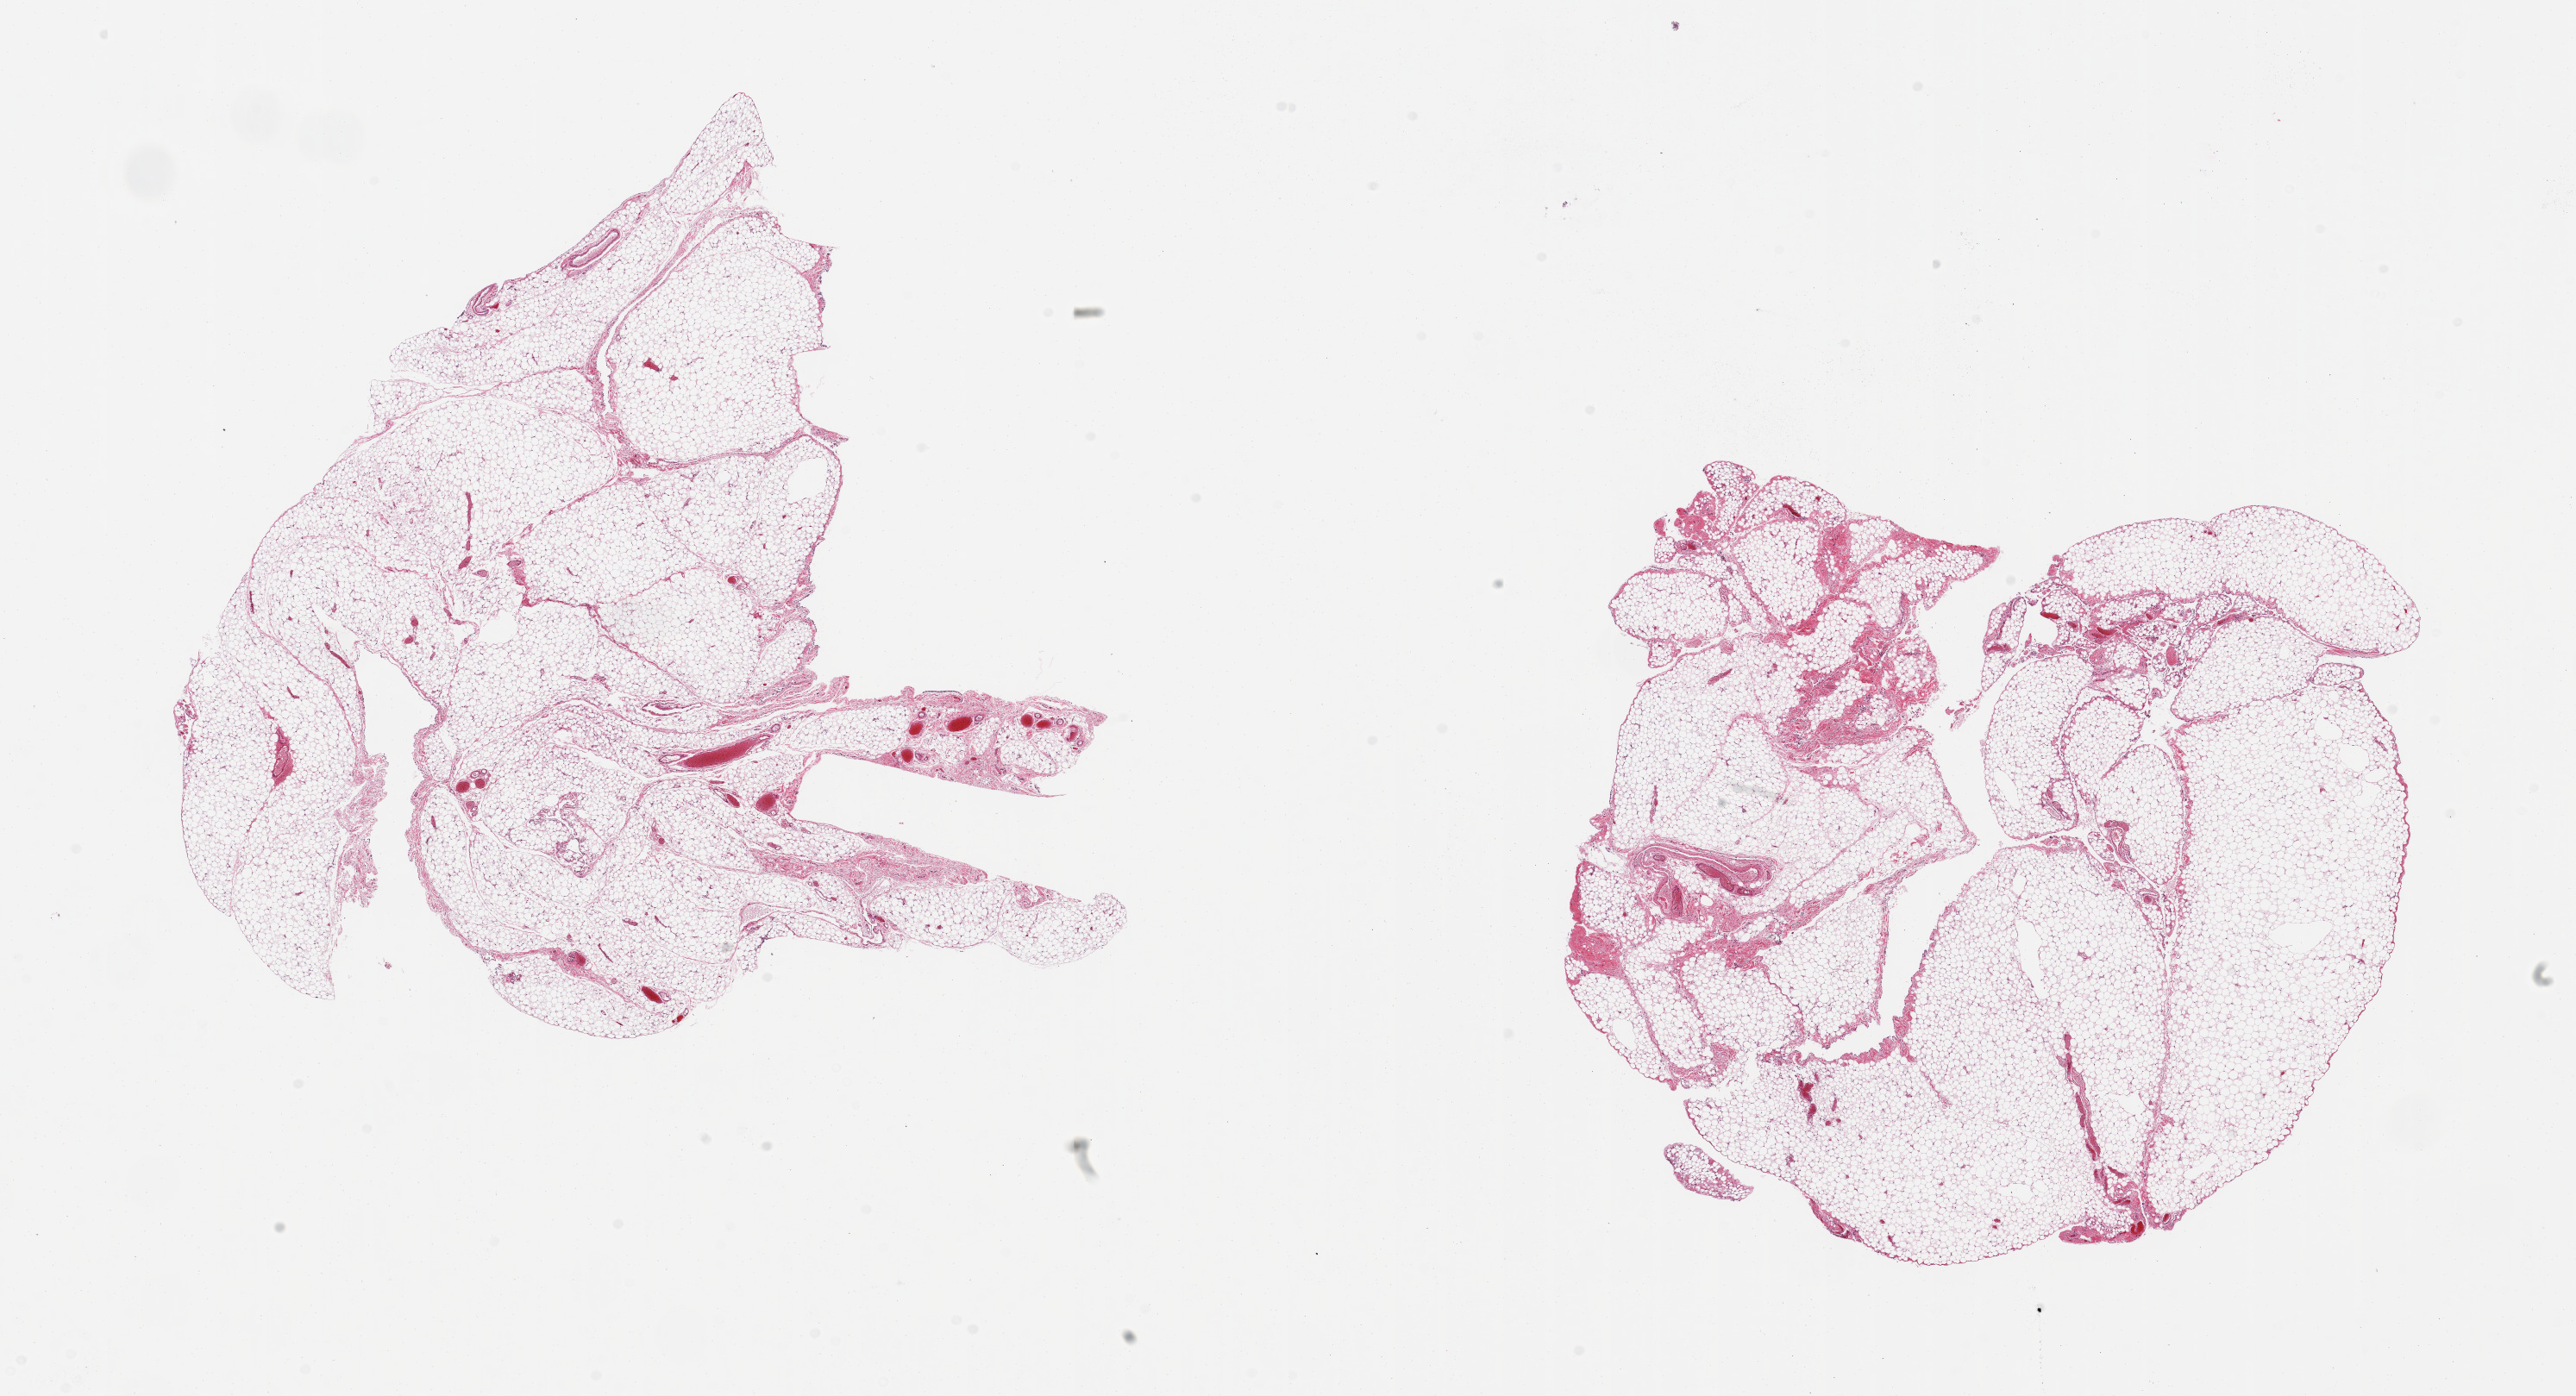
Whole-slide image, H&E stain, shown as a low-resolution overview of the whole scanned area (about 23.6 x 12.8 mm). PAXgene-fixed paraffin-embedded (PFPE) section. Sampled site (target tissue): omentum. Donor tissue sample. Female donor.
Pathologist's review note for this sample: 2 pieces, ~15% prominent fascia/mesothelial hyperplasia/vascular elements.